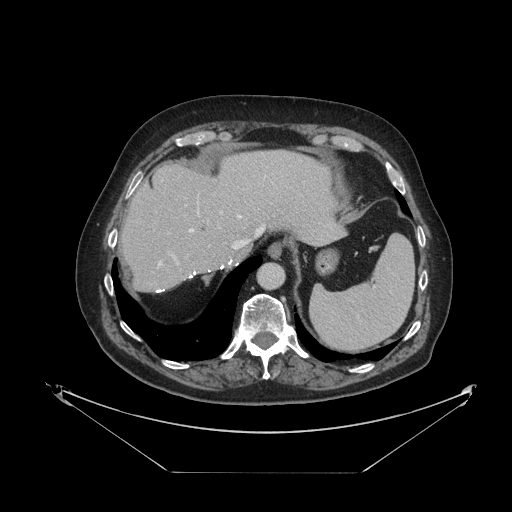
Contrast-enhanced abdominal CT, one axial slice; slice 91 of 121 in the series (ordered by position); 120 kVp; intravenous contrast given; soft-tissue window (W 400 / L 40 HU); 2.5 mm slice thickness; 512 × 512 image matrix, field of view 500 × 500 mm. Male patient, age 68 years. From the clinical record (not read from this slice): diagnosis: colorectal cancer liver metastases, imaged before liver resection; multiple liver metastases: no; largest metastasis: 4 cm; disease in both lobes: no.
Outlined on this slice (outlined manually by an expert reader):
- hepatic veins: bounding box (x1, y1, x2, y2) in pixels: (159, 210, 265, 266)
- liver: (122, 150, 343, 292)
- planned liver remnant (the part of the liver to remain after resection): (121, 150, 342, 292)
- portal vein (with intrahepatic branches): (171, 212, 222, 264)